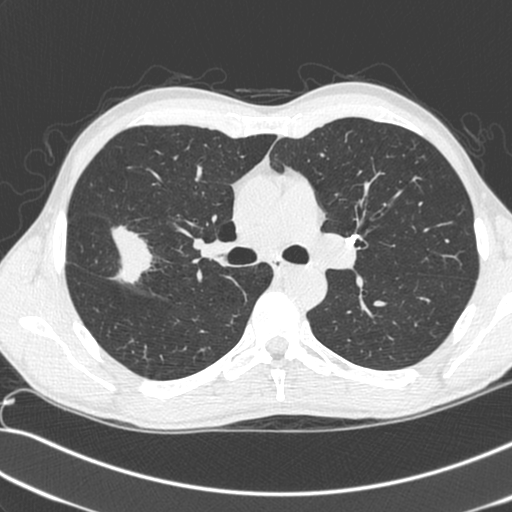
Low-dose screening chest CT, axial slice, first (baseline) screen, lung window (W 1500 / L -600 HU), 1.3 mm slice thickness, standard (soft-tissue) reconstruction kernel (C), slice 94 of 281 in the series. Male participant, aged 55 years at enrolment.
Expert reader's lesion annotation, bounding box <66,217,157,295> (left, top, right, bottom; pixels). Screening reader's record for this exam (one nodule recorded; not confirmed to be the boxed lesion): non-calcified nodule or mass ≥4 mm, right upper lobe, 52 × 39 mm, spiculated (stellate) margins, soft tissue attenuation. Official screen result: positive, change unspecified: nodule(s) >= 4 mm or enlarging nodule(s), mass(es), or other non-specific abnormalities suspicious for lung cancer. Participant outcome: lung cancer diagnosed 25 days after this screen — large cell neuroendocrine carcinoma, right upper lobe, poorly differentiated (G3), stage IIB (AJCC 6th edition), 49 mm at pathology.